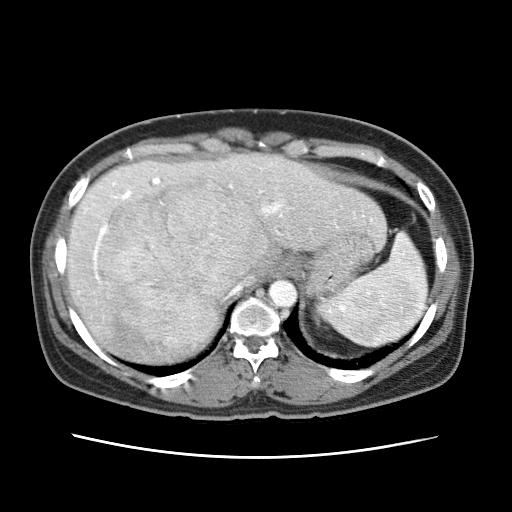
Contrast-enhanced abdominal CT (liver protocol), one axial slice; position 51 of 79 along the scan axis; soft-tissue window (W 400 / L 40 HU); 2.5 mm slice thickness; 512 × 512 image matrix. From the clinical record (not read from this slice): diagnosis: hepatocellular carcinoma (patient treated with transarterial chemoembolisation; whether this scan precedes or follows treatment is not stated here); TNM stage (as recorded): Stage-I.
Annotated regions visible in this slice (semi-automatically segmented with operator editing):
- abdominal aorta: box from (x=269, y=279) to (x=298, y=308) px
- liver parenchyma outside the tumour (the mass and vessels are separate outlines, so this box may not span the whole liver): (x=66, y=154)–(x=383, y=362)
- mass: (x=97, y=177)–(x=268, y=346)
- liver vessels: (x=85, y=177)–(x=373, y=280)